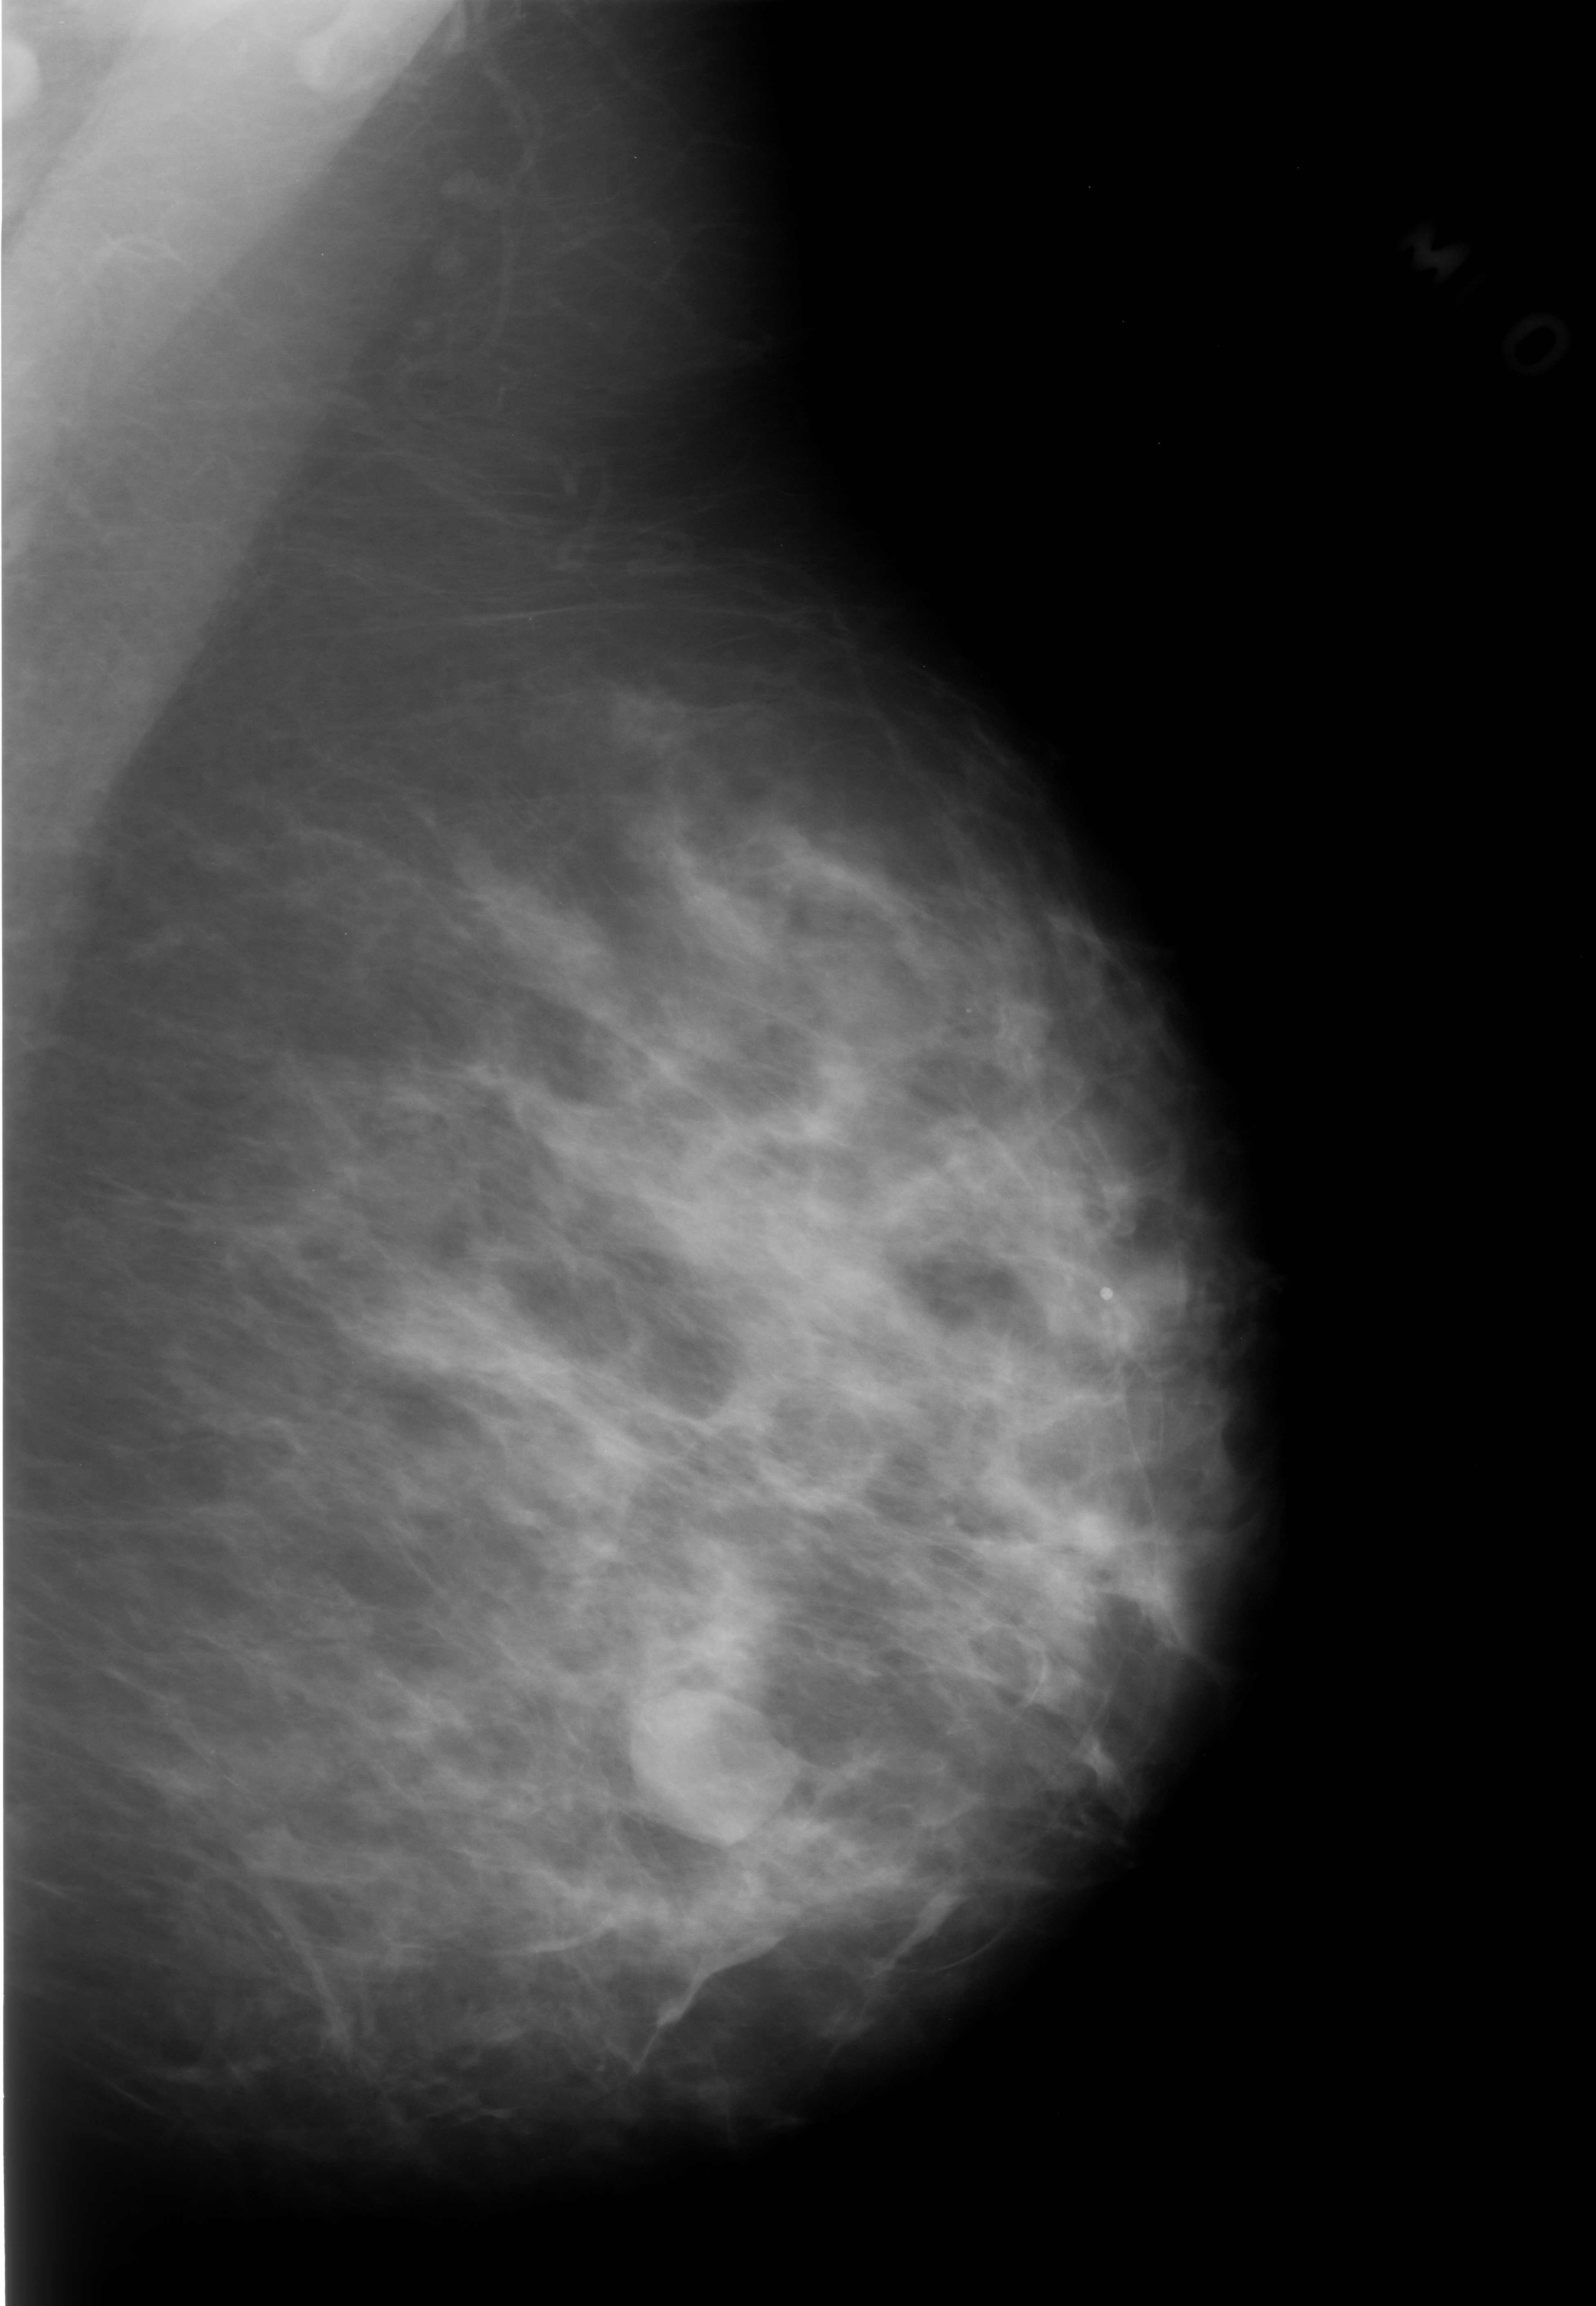
Mammogram (digitized film); left breast; MLO view; breast composition: scattered fibroglandular densities (BI-RADS density category 2 of 4).
- Marked findings (only marked abnormalities are described; nothing is implied about the rest of the image): mass, shape oval, margins circumscribed; BI-RADS assessment category 3; subtlety rating 5 on a 1 (subtle) to 5 (obvious) scale; pathology result (as recorded, not read from the image): benign.